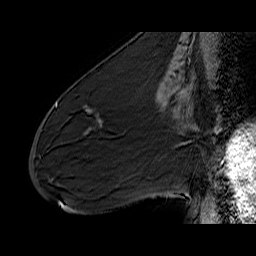
Breast MRI (dynamic contrast-enhanced), one sagittal slice; position 27 of 60 along the scan axis; dynamic contrast-enhanced series, time point 2 of 6 at this slice position (early post-contrast); 1.5 T; TE 6.5 ms, TR 32.9 ms; 4 mm slice thickness; 256 × 256 image matrix, field of view 200 × 200 mm. Female patient. Case-level facts recorded for this patient, not image findings: setting: breast cancer imaged before/during neoadjuvant chemotherapy; receptor status: HER2-positive.
Structures marked on this image (semi-automatic segmentation, software-assisted and operator-edited):
- analysis volume of interest (the breast-tissue region the enhancement analysis was run in; not a lesion): bounding box (x1, y1, x2, y2) in pixels: (72, 88, 133, 137)
- tumour enhancement mask (voxels above the 100 % enhancement threshold inside the analysis volume of interest): (88, 120, 102, 131)